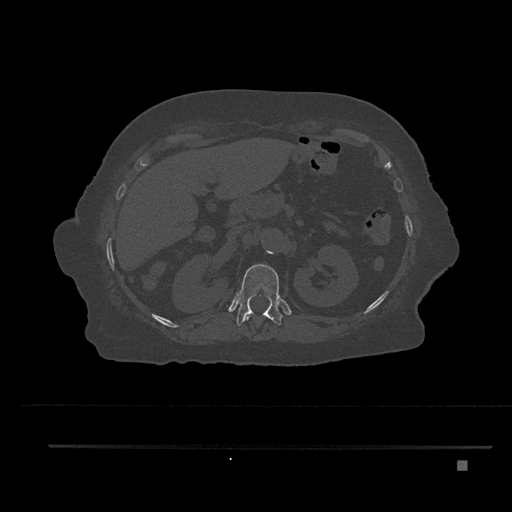
CT including the spine, one axial slice. Slice 270 of 797 in the series (ordered by position). Bone window (W 1800 / L 400 HU). 0.5 mm slice thickness. 512 × 512 image matrix, field of view 437 × 437 mm. Patient: female, 76 years. From the clinical record (not read from this slice): primary cancer: lung.
Annotated regions visible in this slice (semi-automatic segmentation, software-assisted and operator-edited):
- T11 vertebra: bounding box [x1, y1, x2, y2] px = [244, 313, 260, 339]
- T12 vertebra: [236, 264, 283, 326]